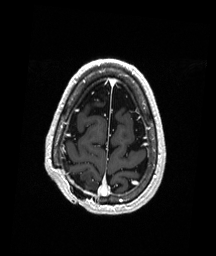
Brain MRI from a brain-tumour surgery series, one axial slice; position 48 of 192 along the scan axis; T1-weighted post-contrast; 1 mm slice thickness; 216 × 256 image matrix, field of view 211 × 250 mm. Case-level facts recorded for this patient, not image findings: histopathology: Astrocytoma; WHO grade: 3; IDH mutation: yes; tumour location: Right Parietal.
Outlined on this slice (expert manual segmentation):
- previous resection cavity: bounding box (x1, y1, x2, y2) in pixels: (68, 173, 85, 188)